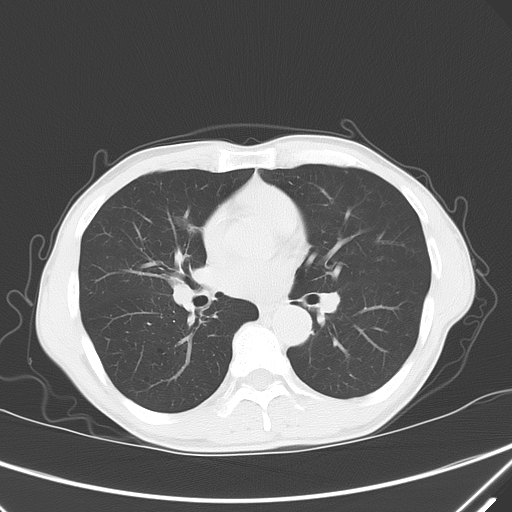
Chest CT, one axial slice; position 35 of 68 along the scan axis; 120 kVp; lung window (W 1500 / L -600 HU); 5 mm slice thickness; 512 × 512 image matrix, field of view 350 × 350 mm. Male patient, age 67 years. From the clinical record (not read from this slice): clinical TNM (as recorded): T1c N0 M0.
Outlined on this slice (bounding box drawn by a radiologist):
- lung tumour (recorded histology: adenocarcinoma): bounding box [x1, y1, x2, y2] px = [169, 209, 199, 242]